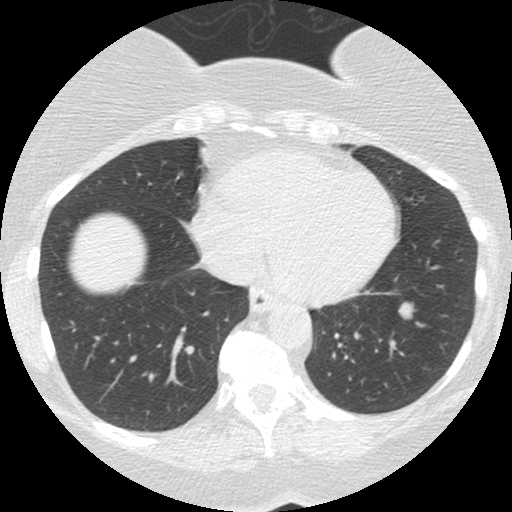
Low-dose screening chest CT, one axial slice; slice 56 of 167 in the series (ordered by position); reconstruction kernel STANDARD; 120 kVp; lung window (W 1500 / L -600 HU); 2.5 mm slice thickness; 512 × 512 image matrix, field of view 300 × 300 mm.
Annotated regions visible in this slice (outlined manually by an expert reader):
- lesion 1 (tumor, lower lobe of left lung): bounding box (x1, y1, x2, y2) in pixels: (399, 303, 413, 318)